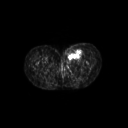
FDG PET of an extremity soft-tissue mass (from a PET/CT study), one axial slice. Position 46 of 267 along the scan axis. 3.27 mm slice thickness. 128 × 128 image matrix, field of view 600 × 600 mm. Patient: female, 24 years. From the clinical record (not read from this slice): histological type: leiomyosarcoma; grade: high; site of the primary tumour: groin.
Structures marked on this image (expert contour drawn on MRI and transferred to this co-registered scan by the dataset authors):
- gross tumour volume including surrounding oedema: bounding box [x1, y1, x2, y2] px = [62, 47, 82, 64]
- gross tumour volume (mass): [68, 49, 81, 58]